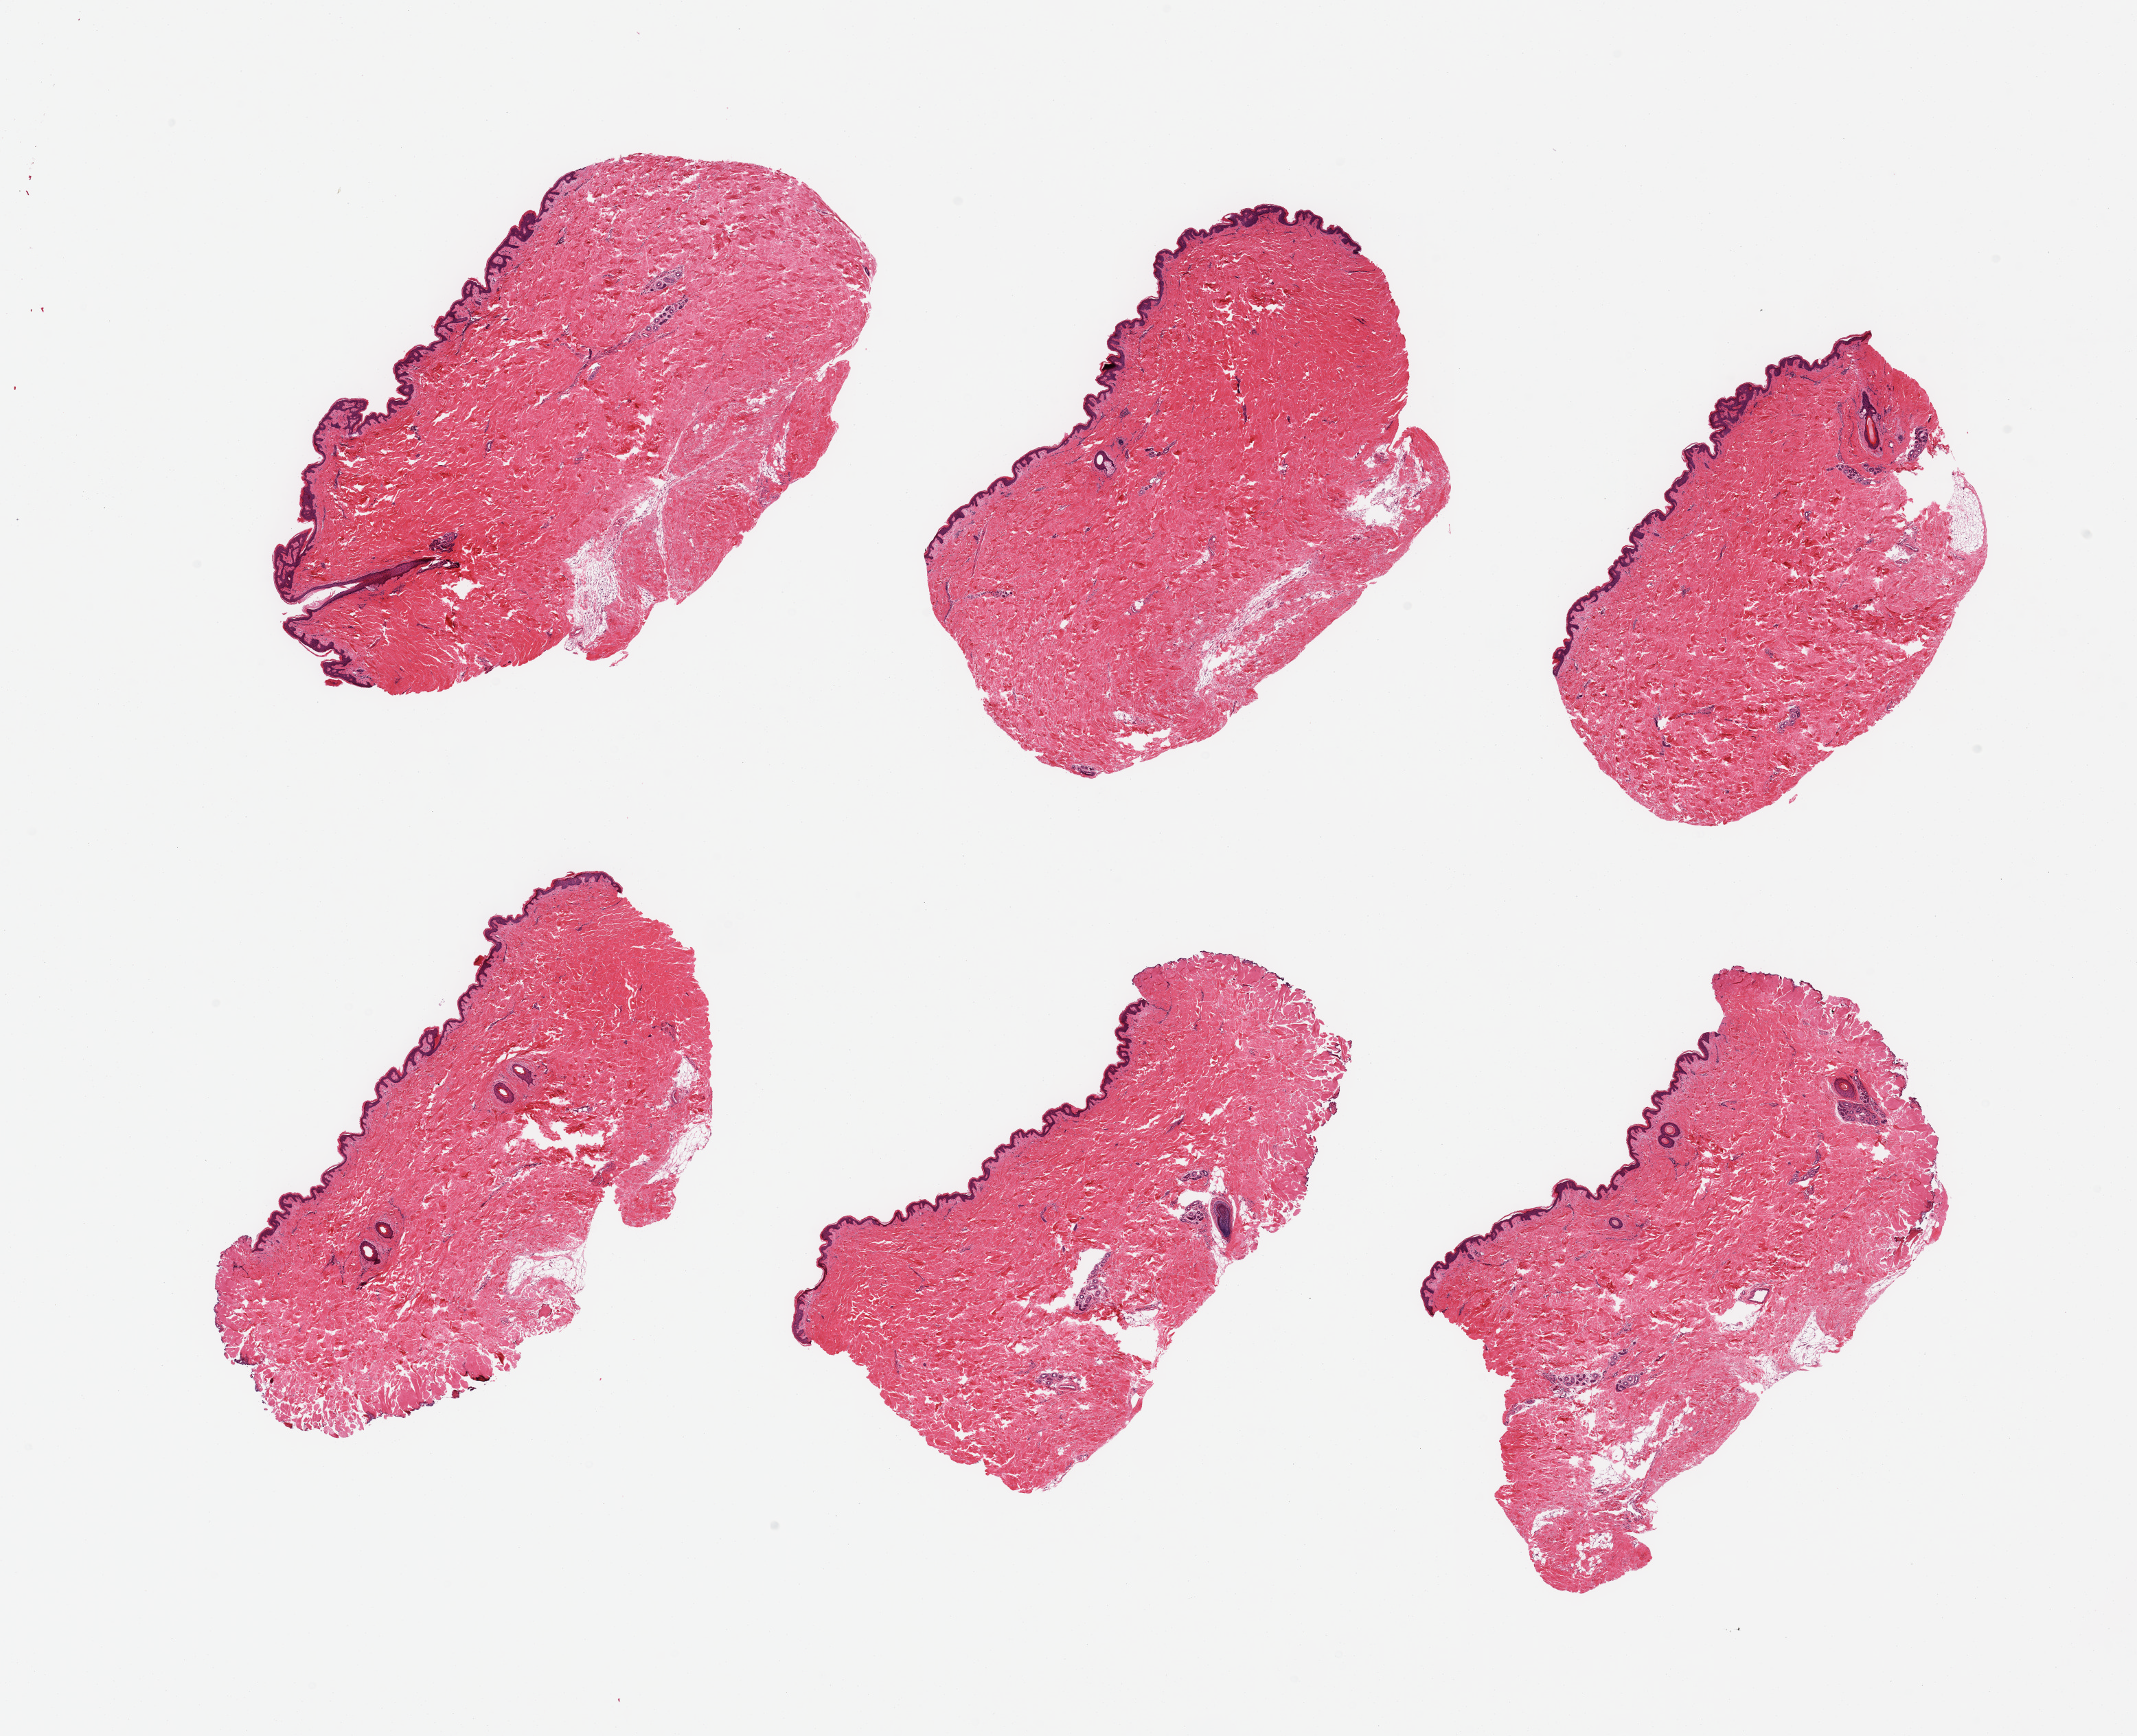
Hematoxylin and eosin (H&E) whole-slide image — whole scanned area (about 24.6 x 20.0 mm) shown as a low-resolution overview; PAXgene-fixed paraffin-embedded (PFPE) section; target tissue: skin of suprapubic region; tissue donor sample. Male donor.
Reviewer comment on this tissue sample: 6 pieces, no significant dermal fat; squamous mucosa is 30-35 microns.